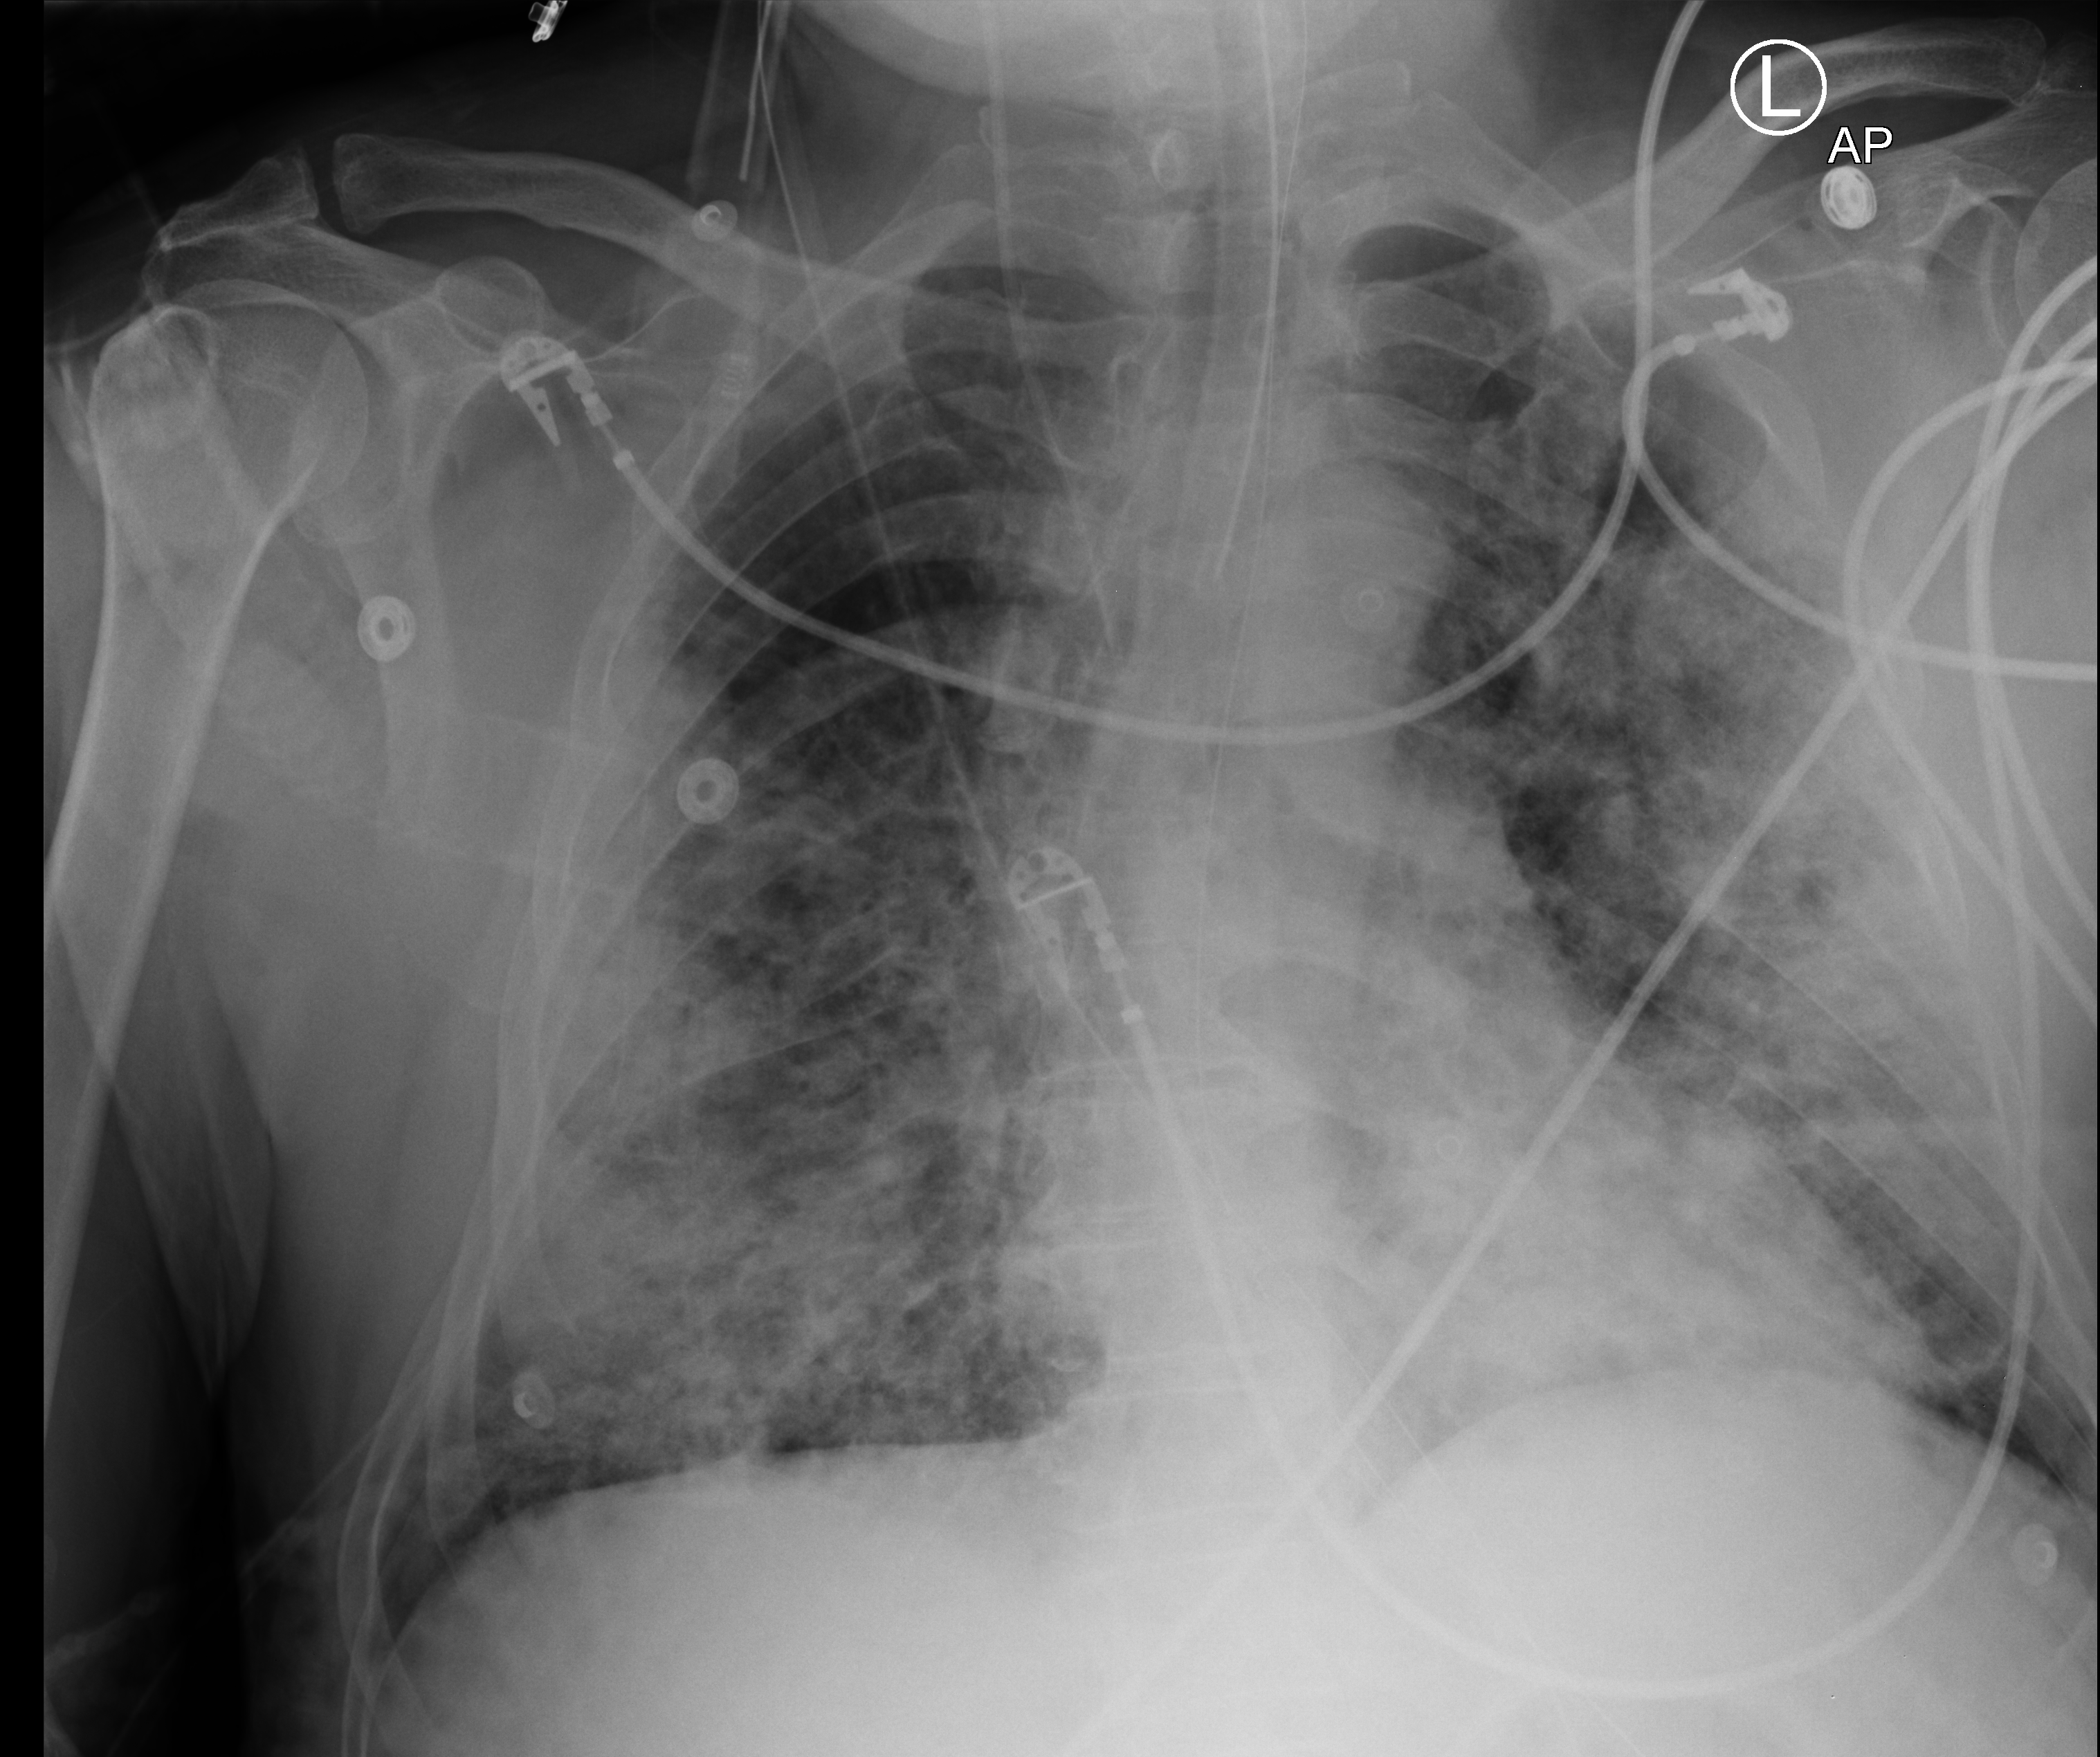
Bedside chest radiograph (computed radiography), anteroposterior (AP) projection. Patient hospitalised with COVID-19; male, aged 60–74 years.
Hospital-stay facts (about this admission, not read from this image; timing relative to this image not recorded):
- mechanically ventilated during this hospital stay: yes
- diabetes (admission record): yes
- admitted to intensive care during this hospital stay: yes